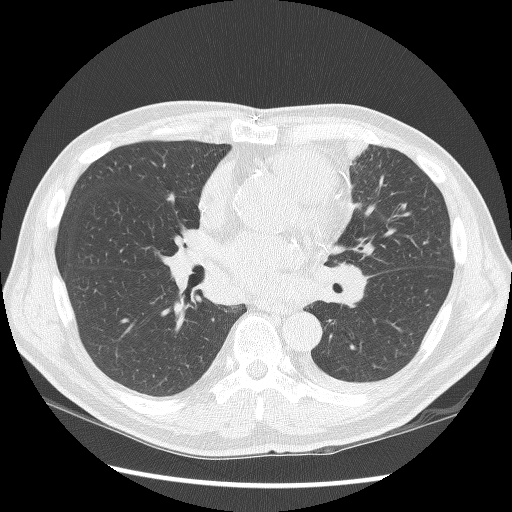
Chest CT (low-dose screening protocol), one axial image, second screening round (one year after baseline), lung window (W 1500 / L -600 HU). Male, age 64 years at enrolment. Former smoker at enrolment.
Lesion marked by an expert reader, bounding box (x1, y1, x2, y2) in pixels: (307, 120, 400, 276). Screening reader's record for this exam: no non-calcified nodule ≥4 mm recorded. Participant outcome: lung cancer diagnosed 24 days after this screen — small cell carcinoma, NOS, left upper lobe, stage IV (AJCC 6th edition), 100 mm at pathology.